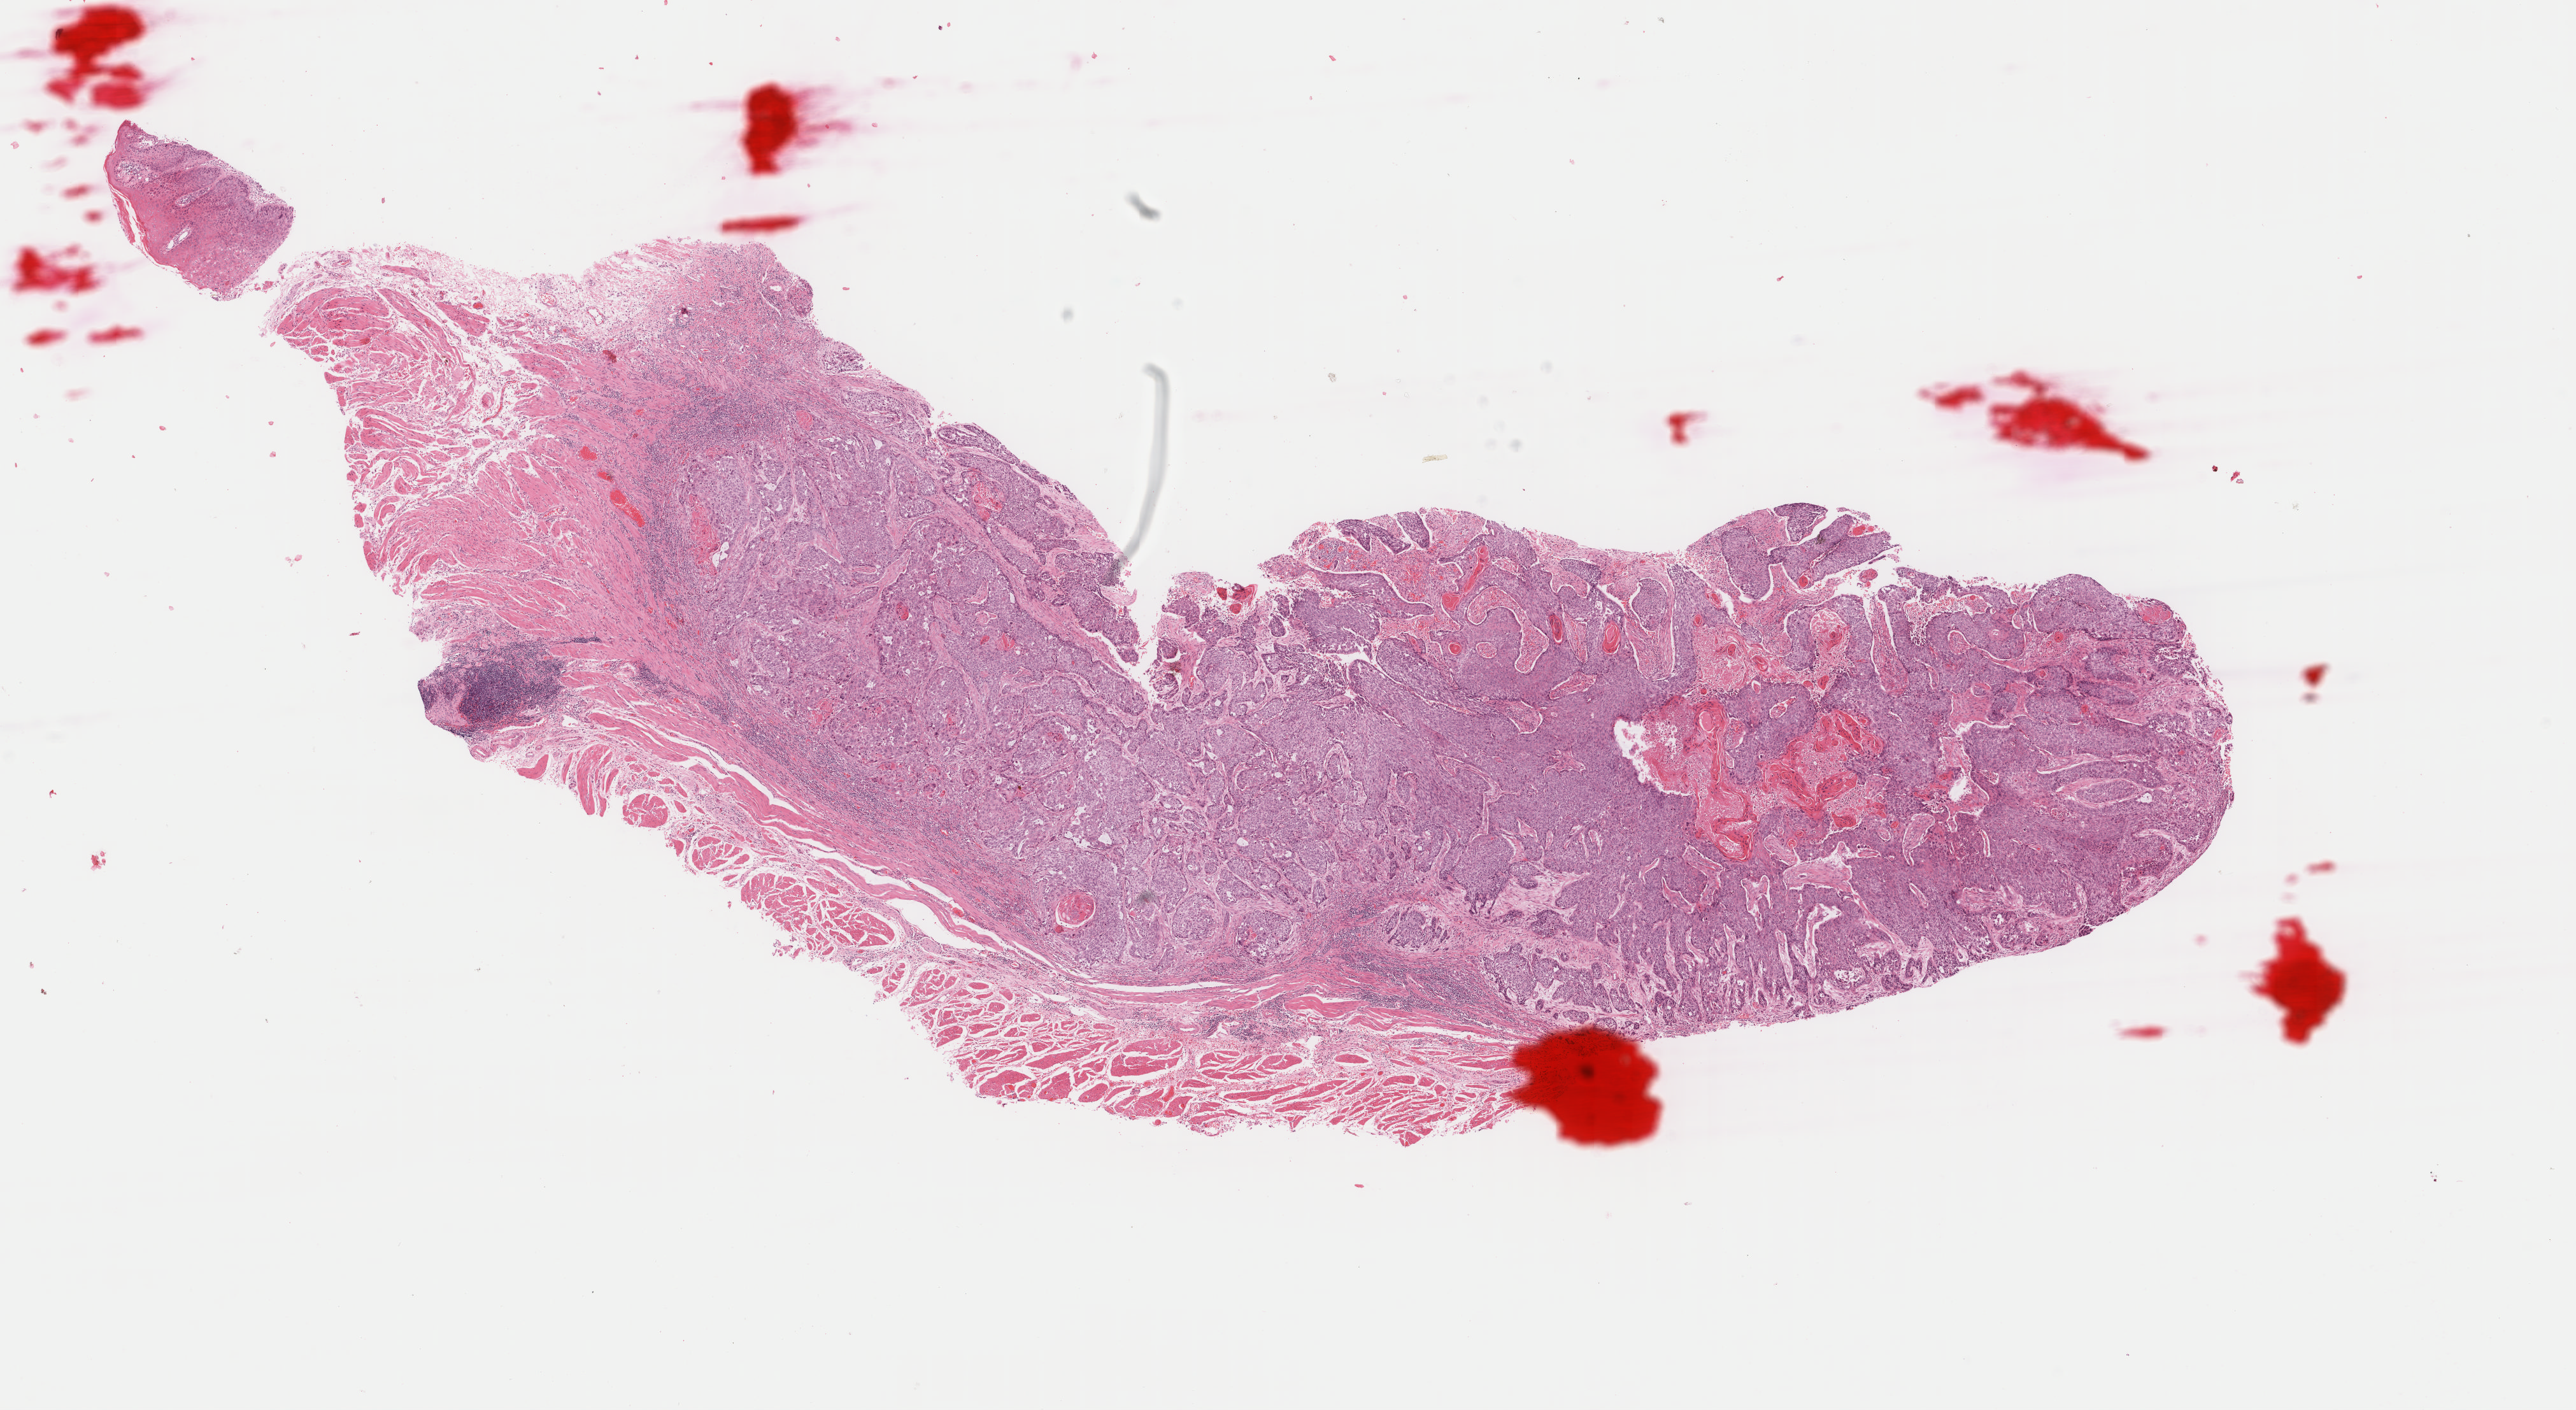
H&E-stained whole-slide image, a low-resolution overview of the entire scanned area, about 16.1 x 8.8 mm; FFPE section; primary tumour sample from the esophagus. Patient: male, age at initial diagnosis 54 years. Histologic grade: G2 (moderately differentiated).
* histologic diagnosis: Squamous cell carcinoma, keratinizing, NOS (lower third of esophagus)
* TNM: T2 N0 M0
* lymph nodes positive (case pathology): 0 of 7 examined
* AJCC pathologic stage: IIA (7th edition)